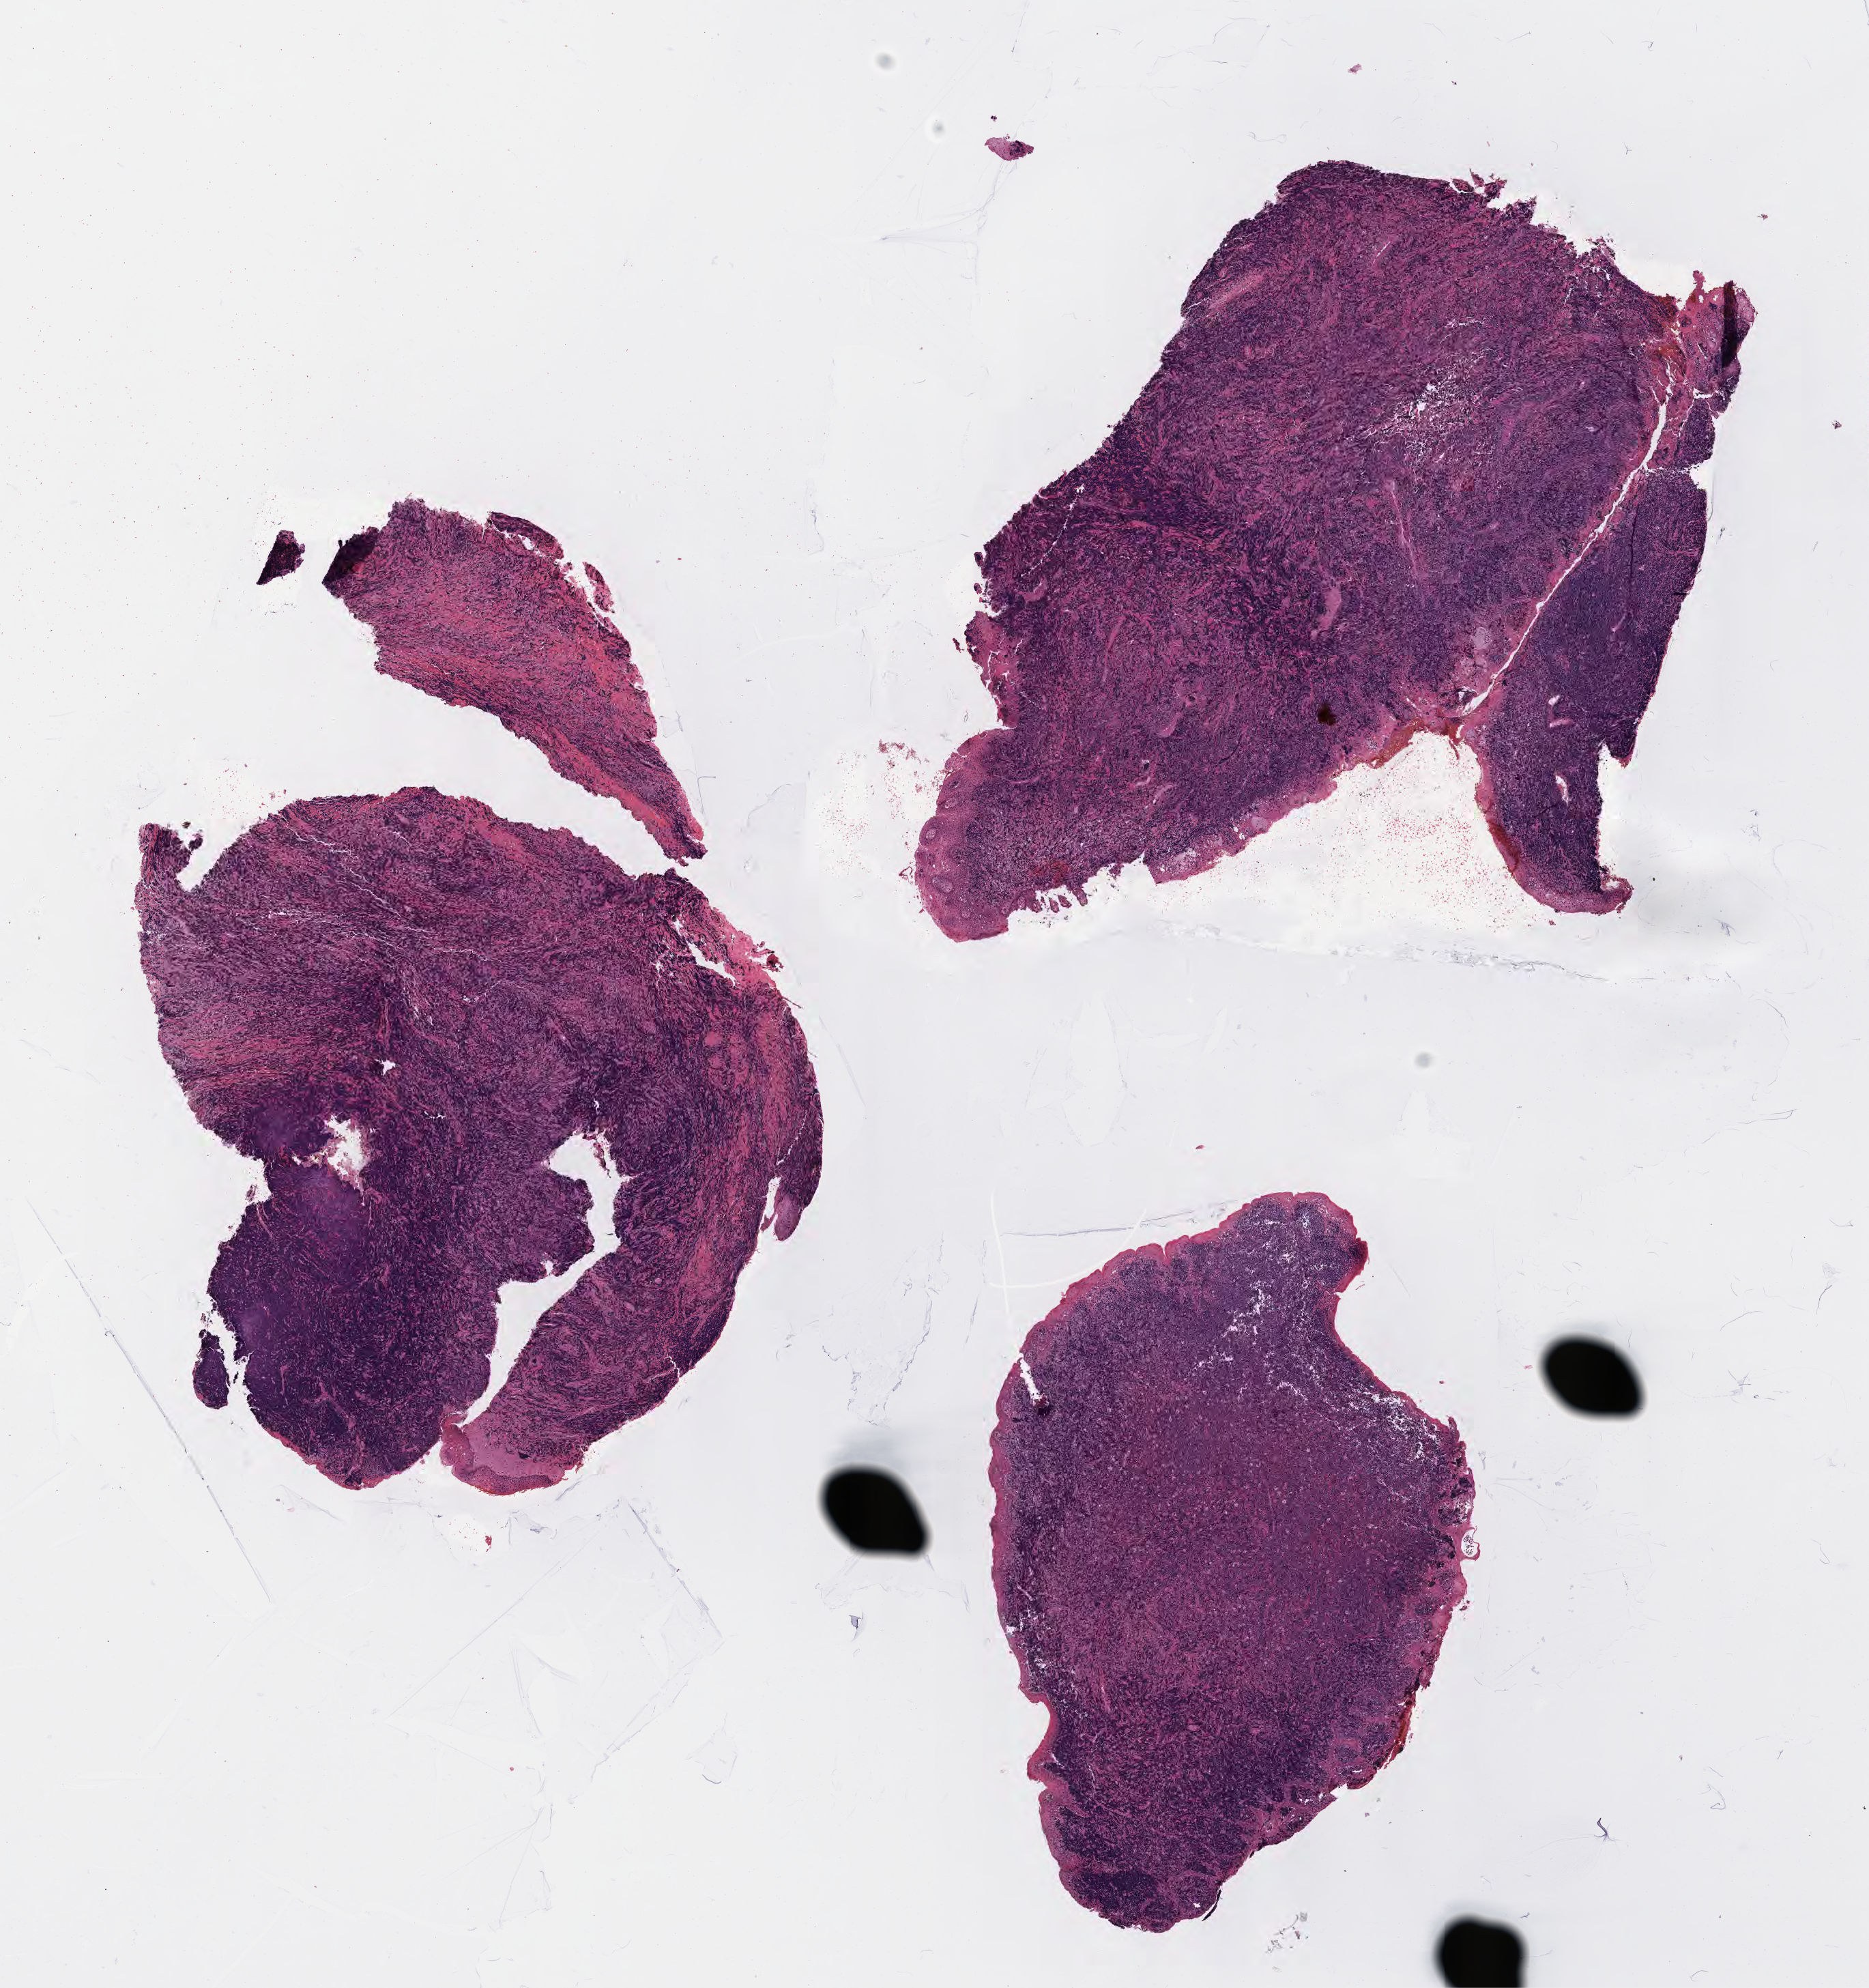
Whole-slide image, H&E stain, shown as a low-resolution overview of the whole scanned area (about 11.1 x 11.8 mm). Specimen: tumor tissue. Site: cranium. Patient: male, age at initial diagnosis 6 years.
• histologic diagnosis: Burkitt lymphoma, NOS